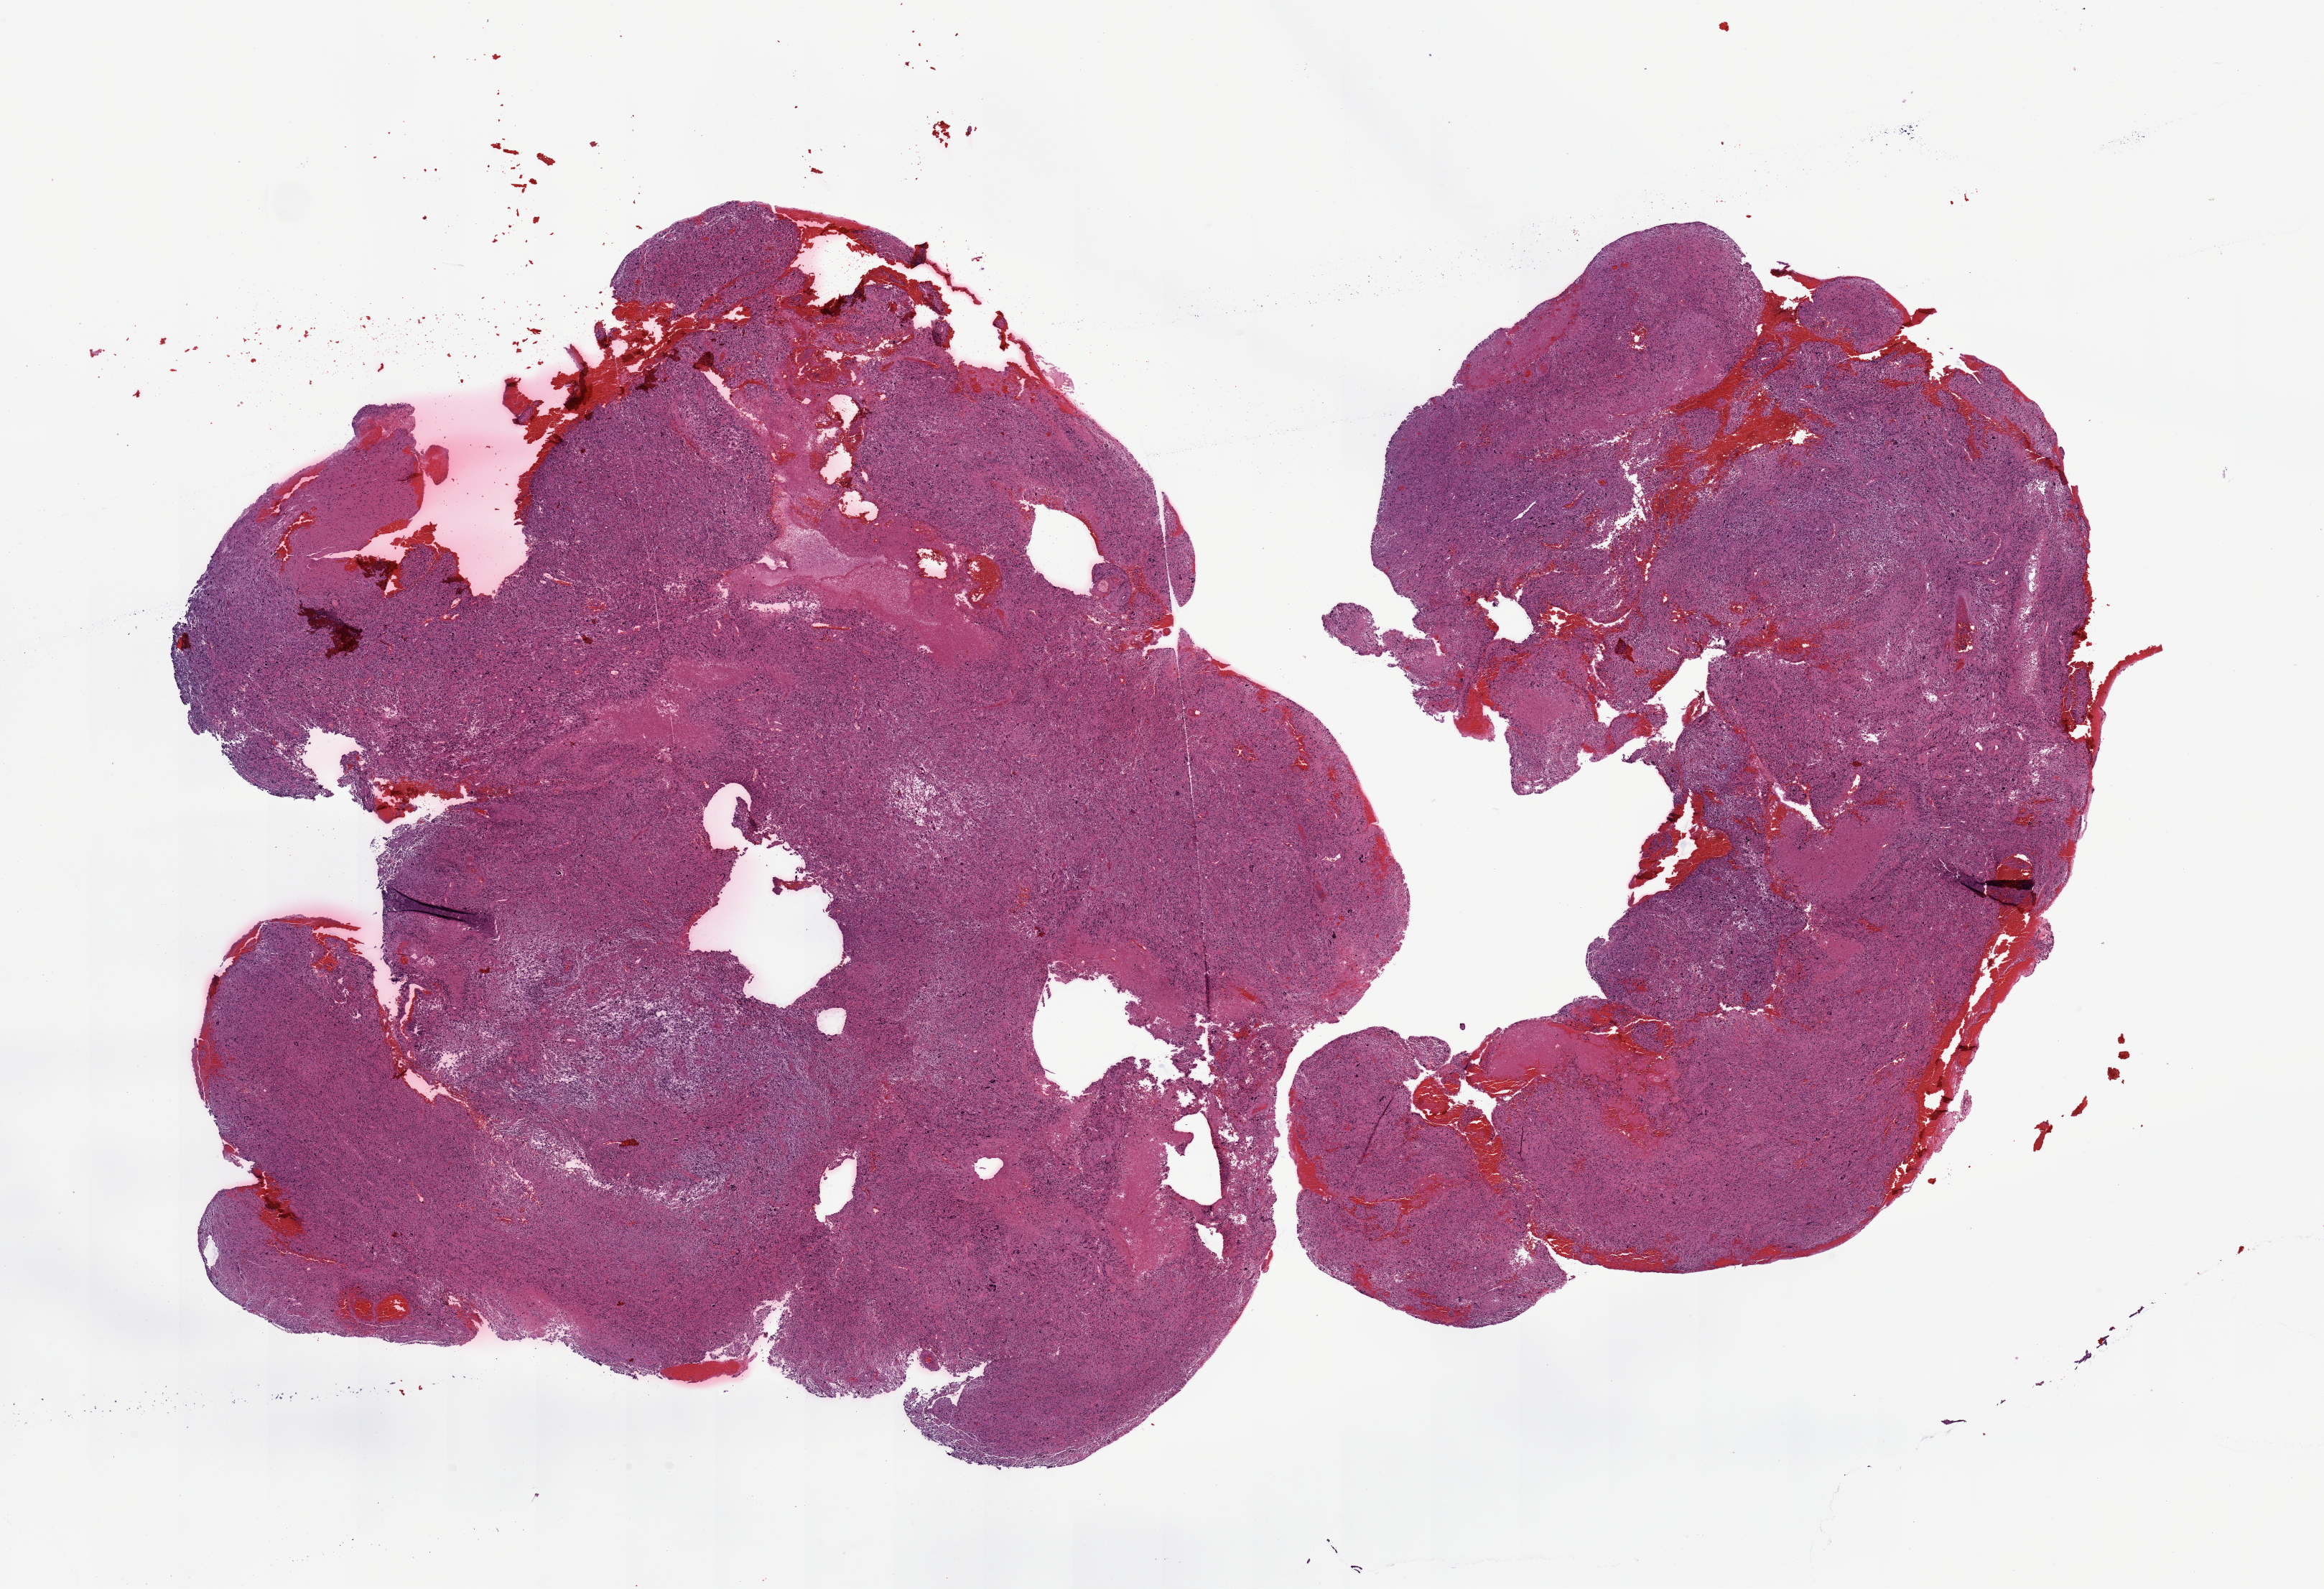
Whole-slide histology image, H&E, a low-resolution overview of the entire scanned area, about 25.6 x 17.5 mm, brain, tumour tissue. Patient: male, age 43 years.
- diagnosis: Glioblastoma
- primary tumour site (as recorded): parietal lobe